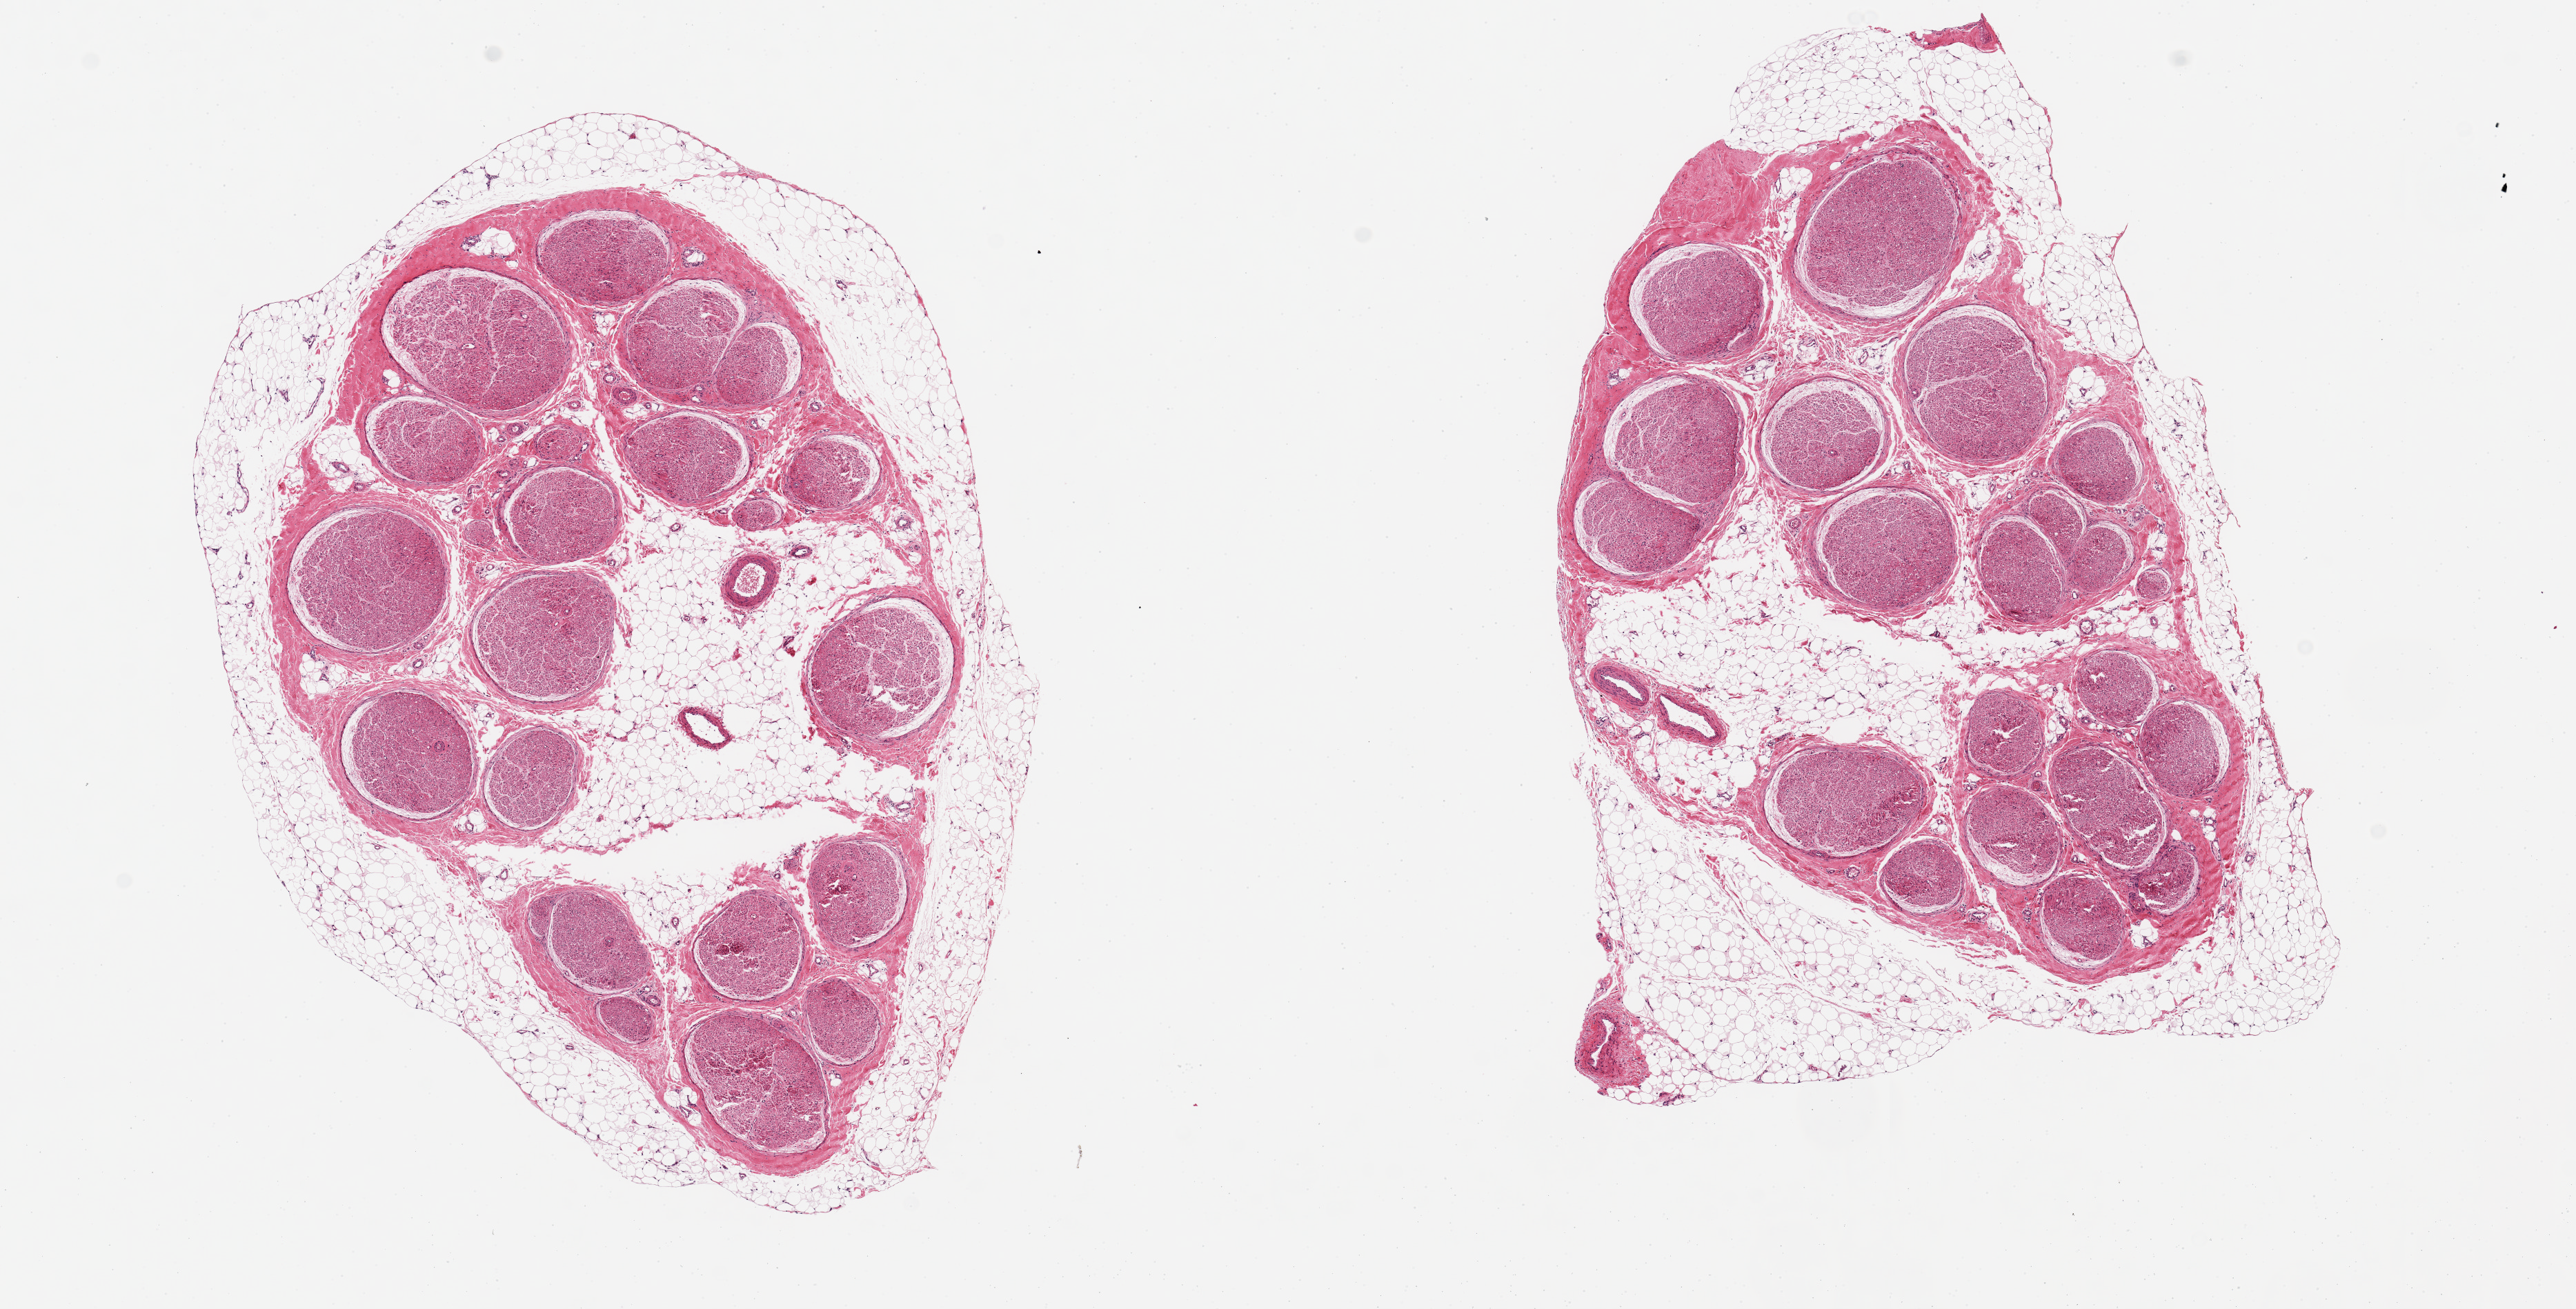
Digitized H&E-stained section, a low-resolution overview of the entire scanned area, about 14.8 x 7.5 mm (from a 20x scan); PAXgene-fixed paraffin-embedded (PFPE) section; section of tibial nerve (target tissue); tissue donor sample. Female donor.
Review note (as recorded): 2 ~6x4.5mm aliquots, both with ~6mm rim of fat.